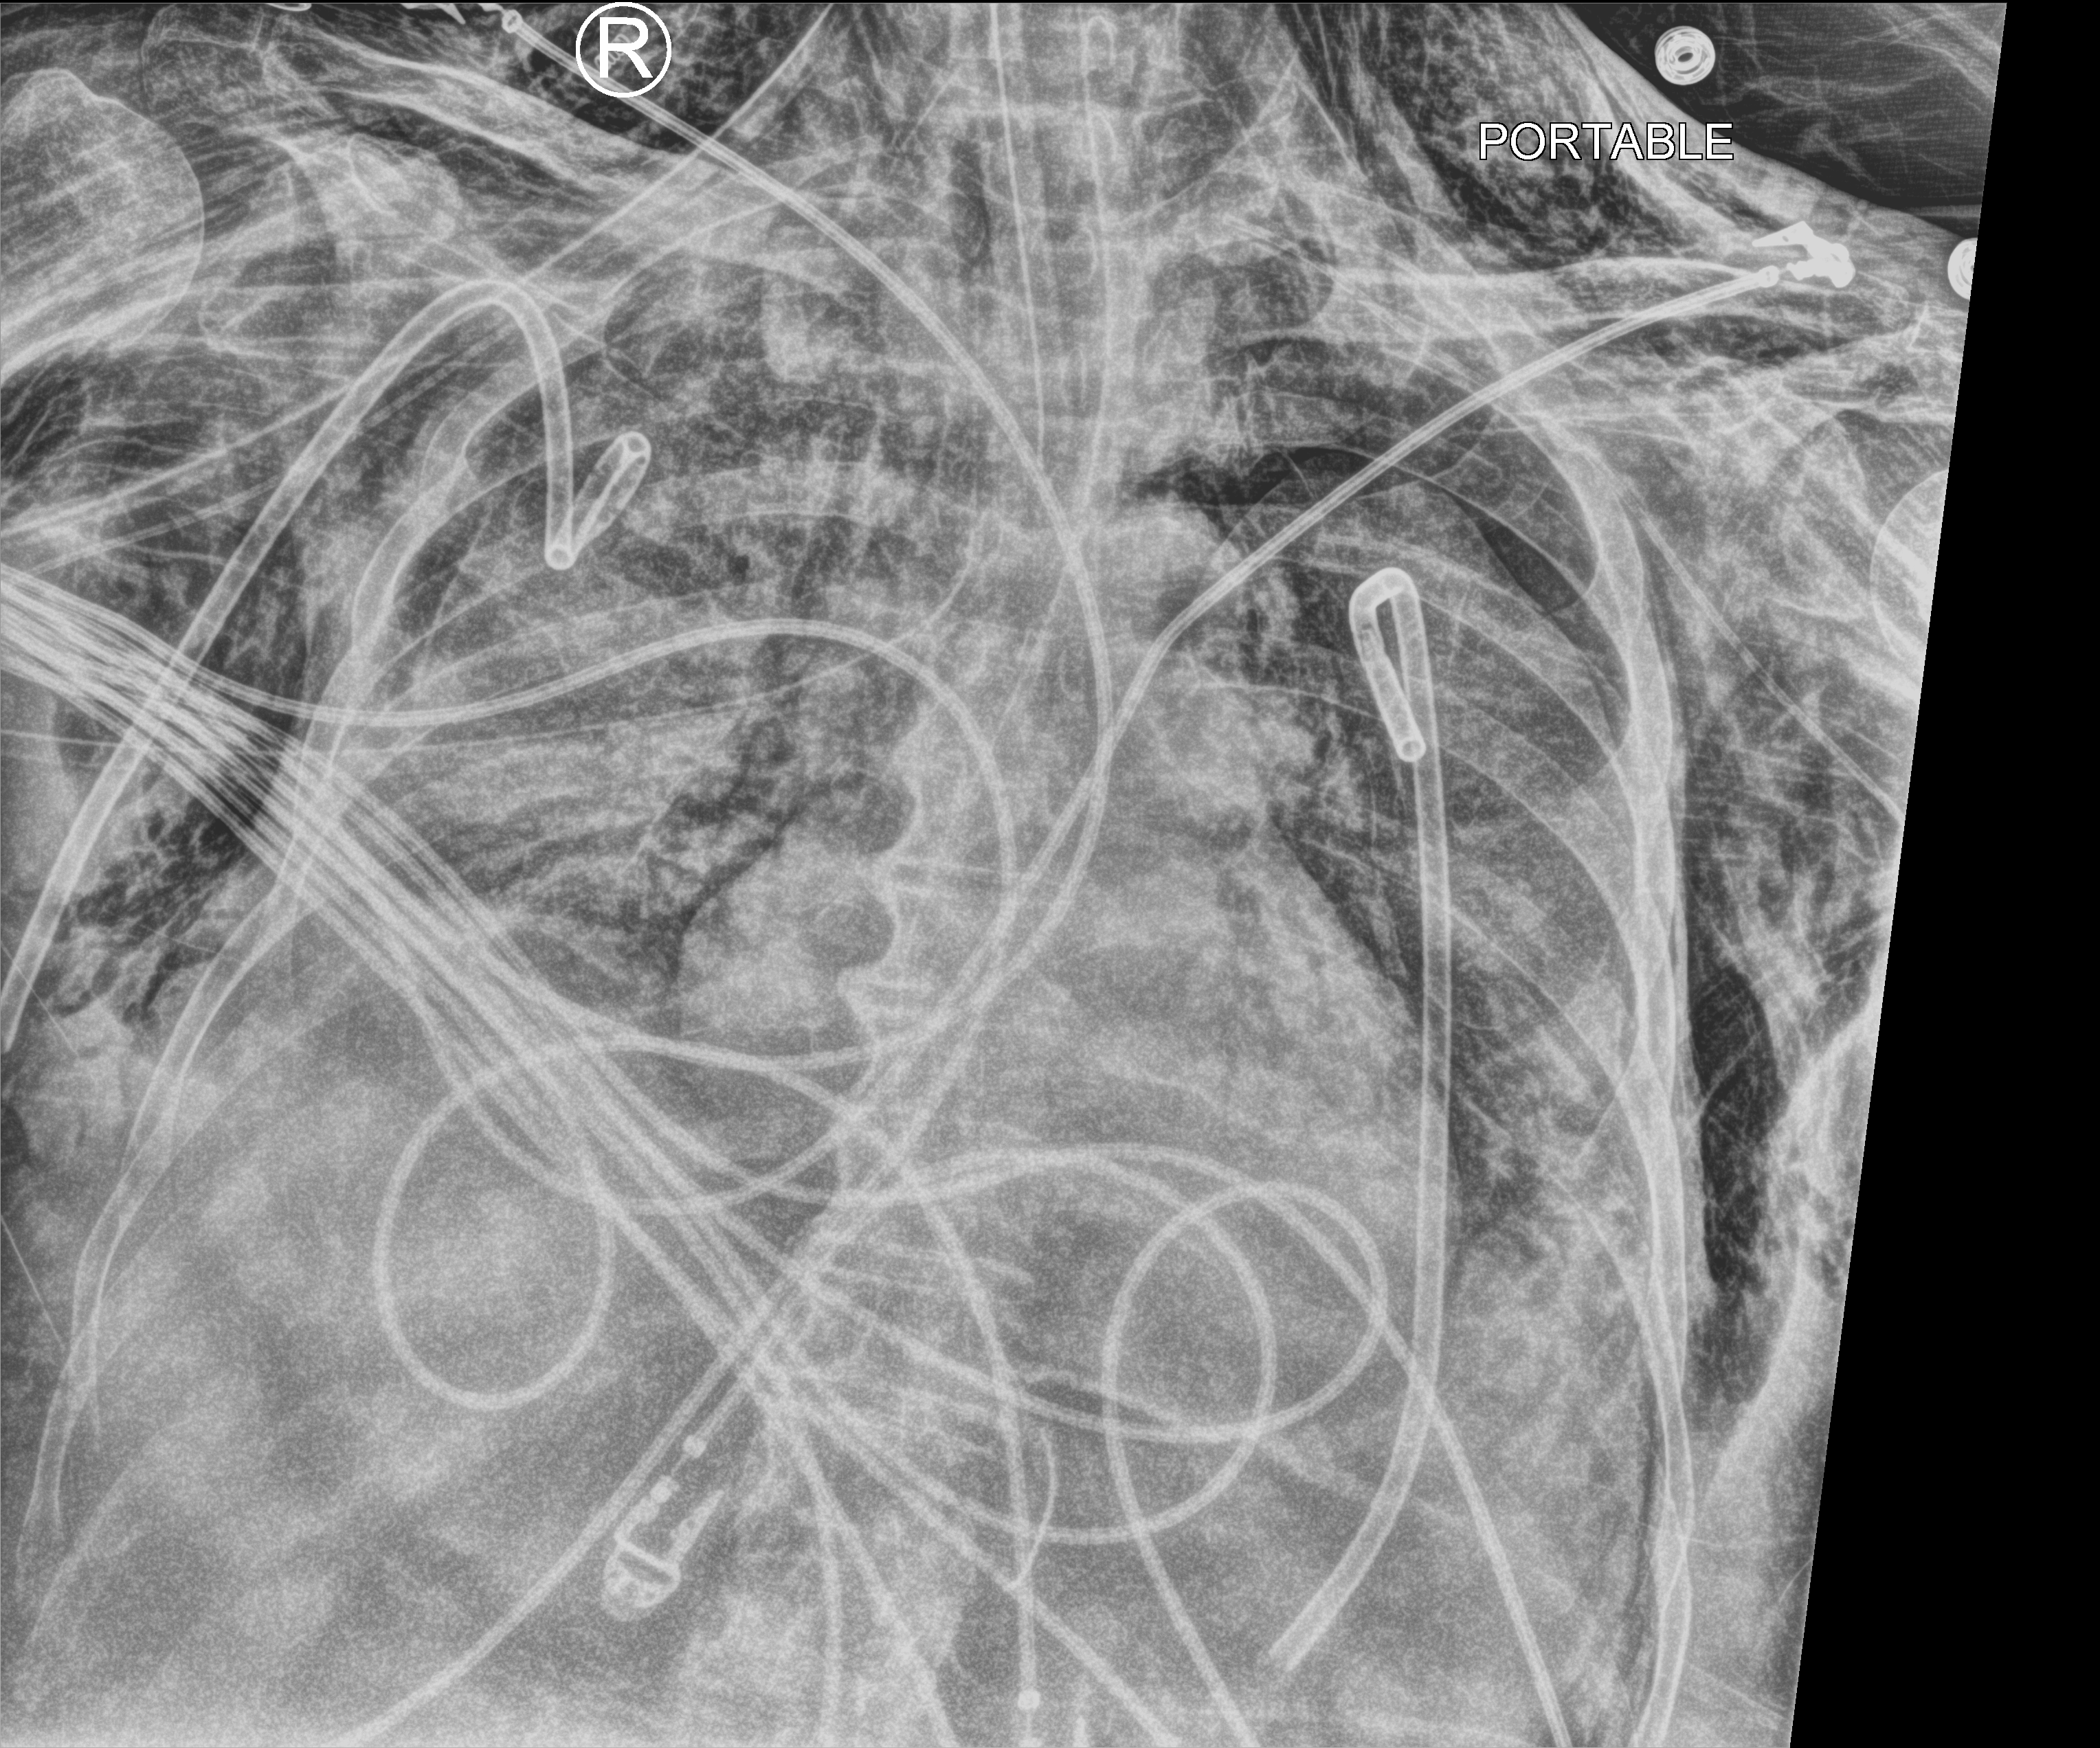
Portable chest radiograph, anteroposterior (AP) projection. Male patient hospitalised with COVID-19, age 75–90 years.
Admission-level facts for this patient (not findings on this image; timing relative to this image not recorded):
- admitted to intensive care during this hospital stay: yes
- mechanically ventilated during this hospital stay: yes
- length of hospital stay: 30 days